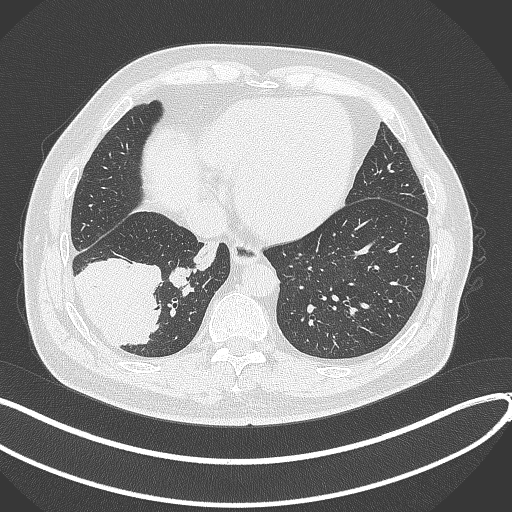
Chest CT, one axial slice; slice 97 of 360 in the series (ordered by position); reconstruction kernel B70f; 120 kVp; lung window (W 1500 / L -600 HU); 1 mm slice thickness; 512 × 512 image matrix, field of view 400 × 400 mm. Male patient, age 59 years.
Outlined on this slice (rectangle marked by the reading radiologist):
- lung tumour (recorded histology: adenocarcinoma): bounding box <69,252,164,348> (left, top, right, bottom; pixels)